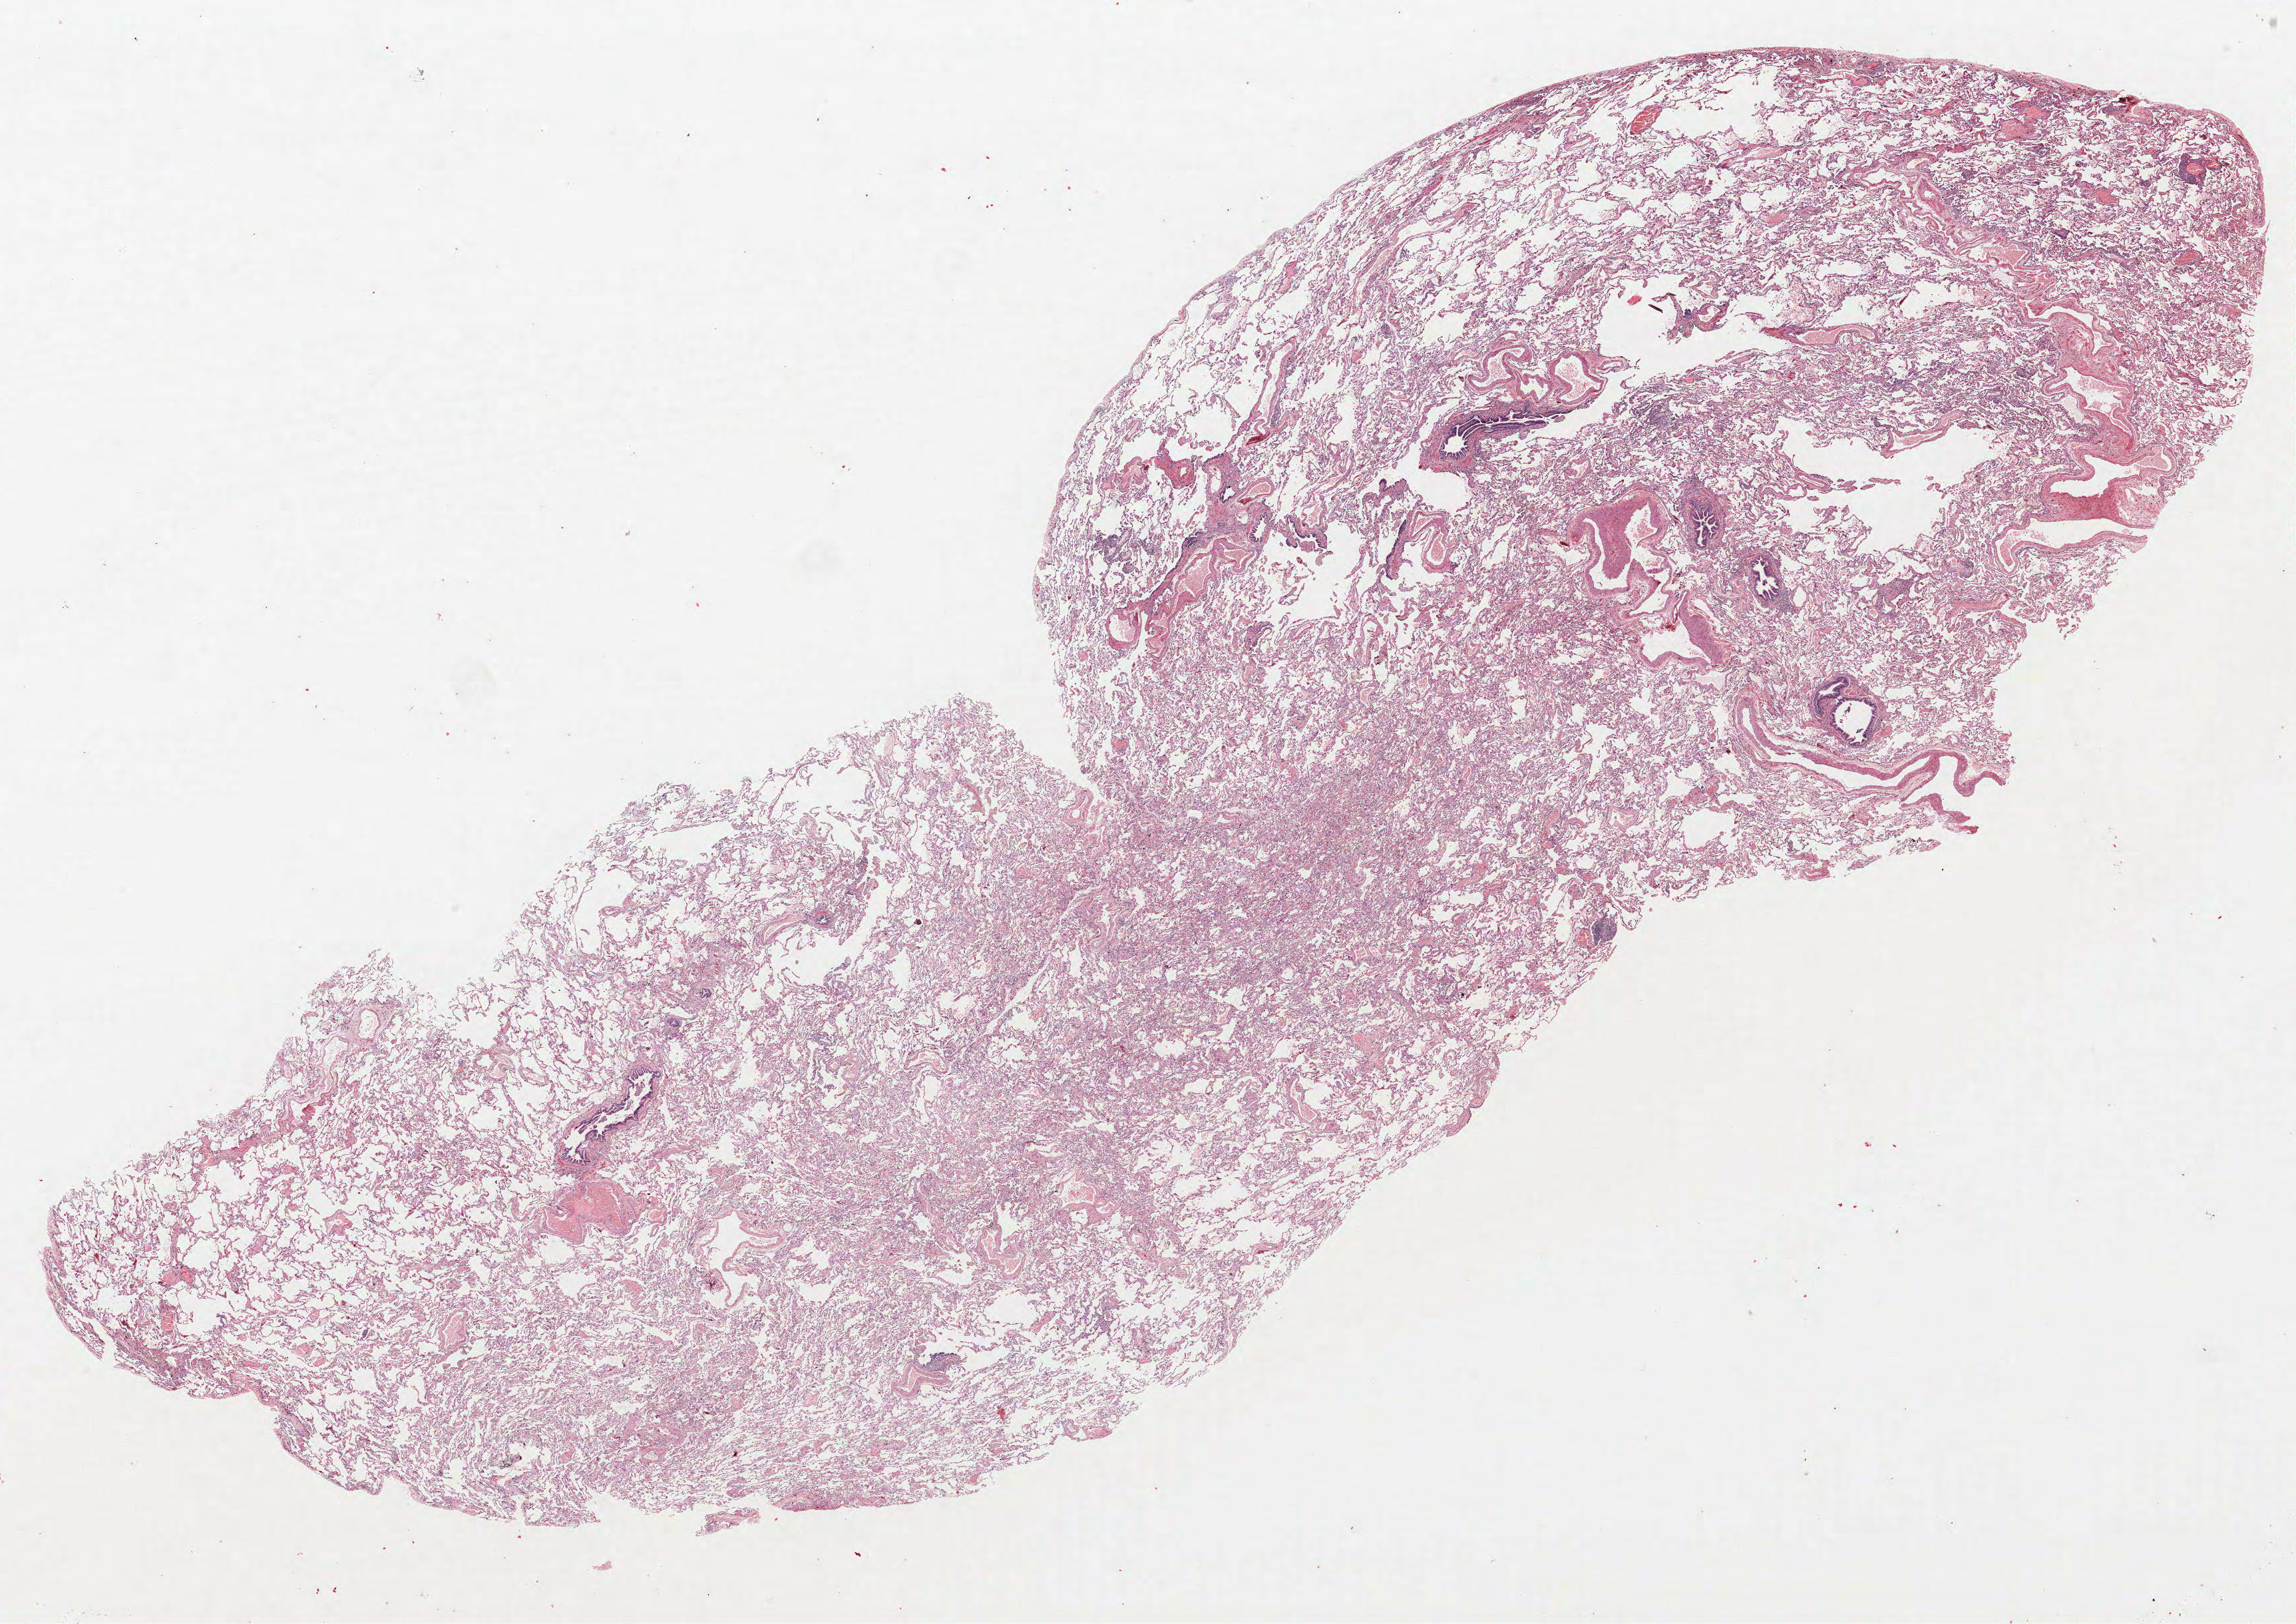
Hematoxylin and eosin (H&E) stained whole-slide image — whole scanned area (about 27.6 x 19.5 mm, from a 40x scan) shown as a low-resolution overview; formalin-fixed paraffin-embedded (FFPE) section; lung. Male, age 55 at enrolment. Grade: moderately differentiated (G2).
• tumour size (pathology): 15 mm
• primary tumour location (clinical record): right upper lobe
• stage (AJCC 6th edition): IA
• participant's lung-cancer diagnosis: Acinar cell carcinoma
• ICD-O-3 topography: upper lobe of lung (C34.1)
• note: participant had 2 primary lung cancers recorded; fields above describe the first